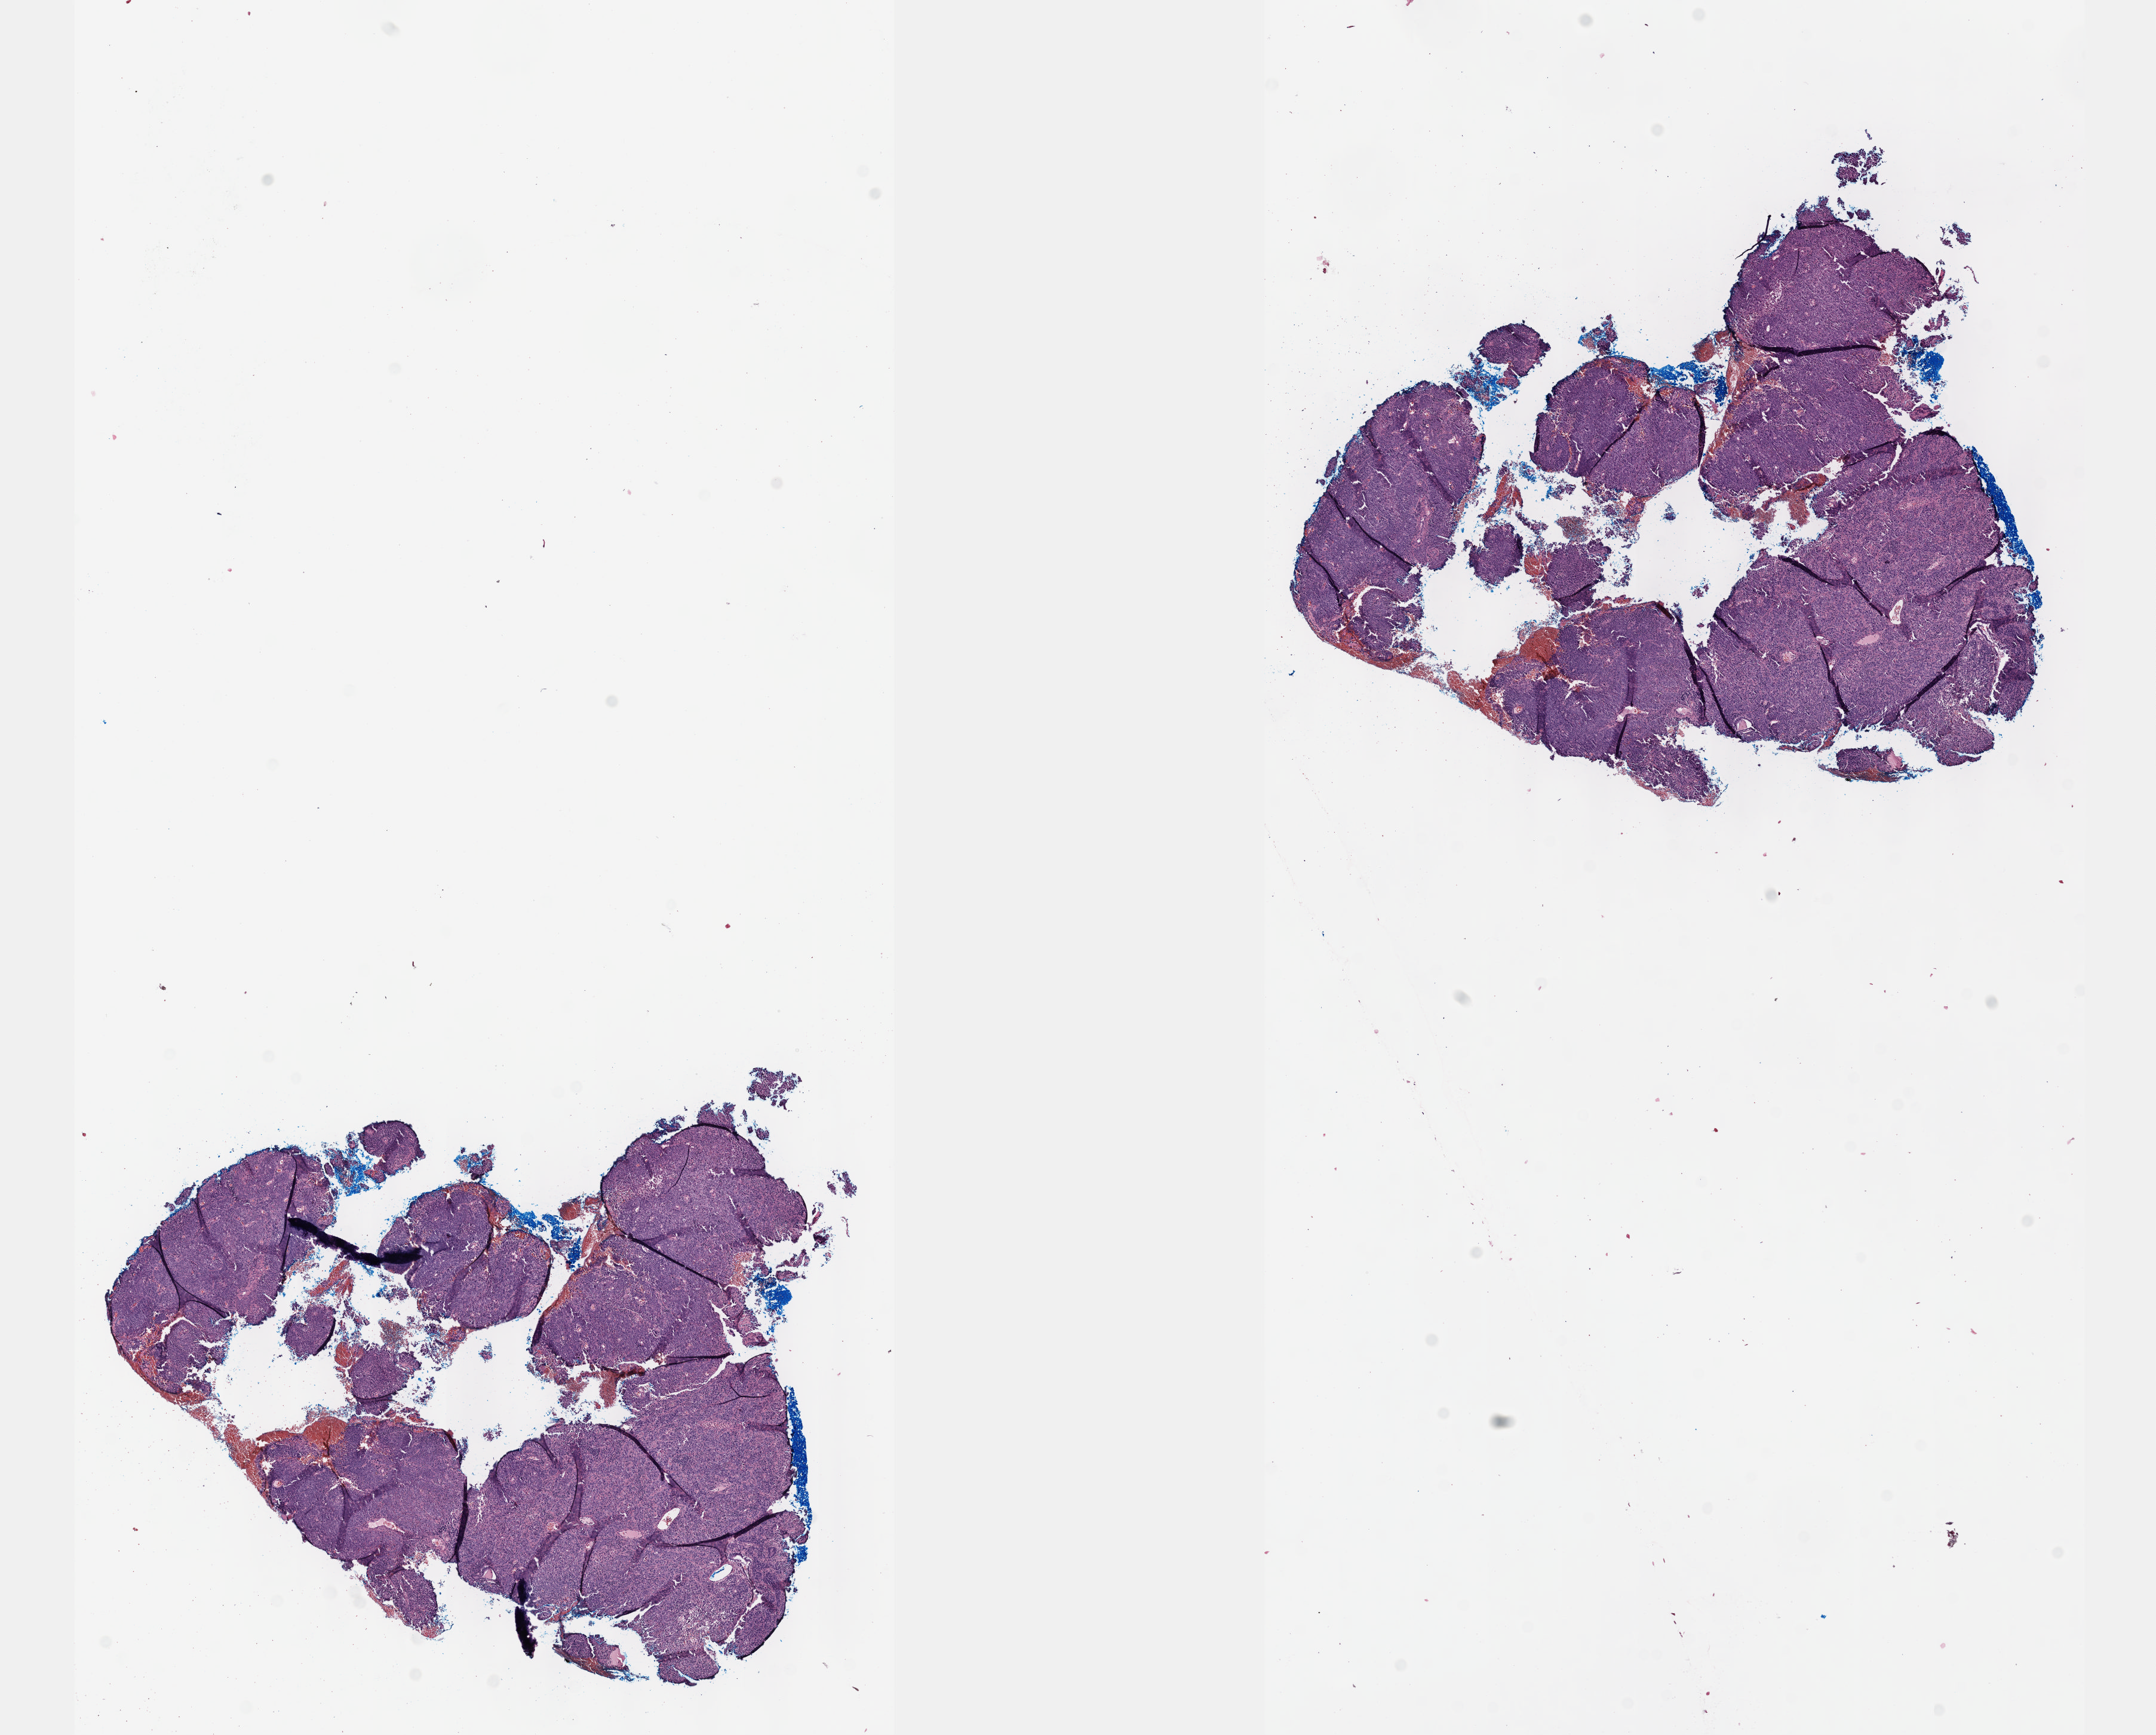
H&E-stained whole-slide image, whole scanned area (about 14.6 x 11.7 mm, slide scanned at 40x) shown as a low-resolution overview. Formalin-fixed paraffin-embedded (FFPE) diagnostic section. Sample: primary tumour, cervix. Female, age 38 years at initial diagnosis. Histologic grade: G2 (moderately differentiated).
Histologic diagnosis: Squamous cell carcinoma, NOS. FIGO stage: IIB.